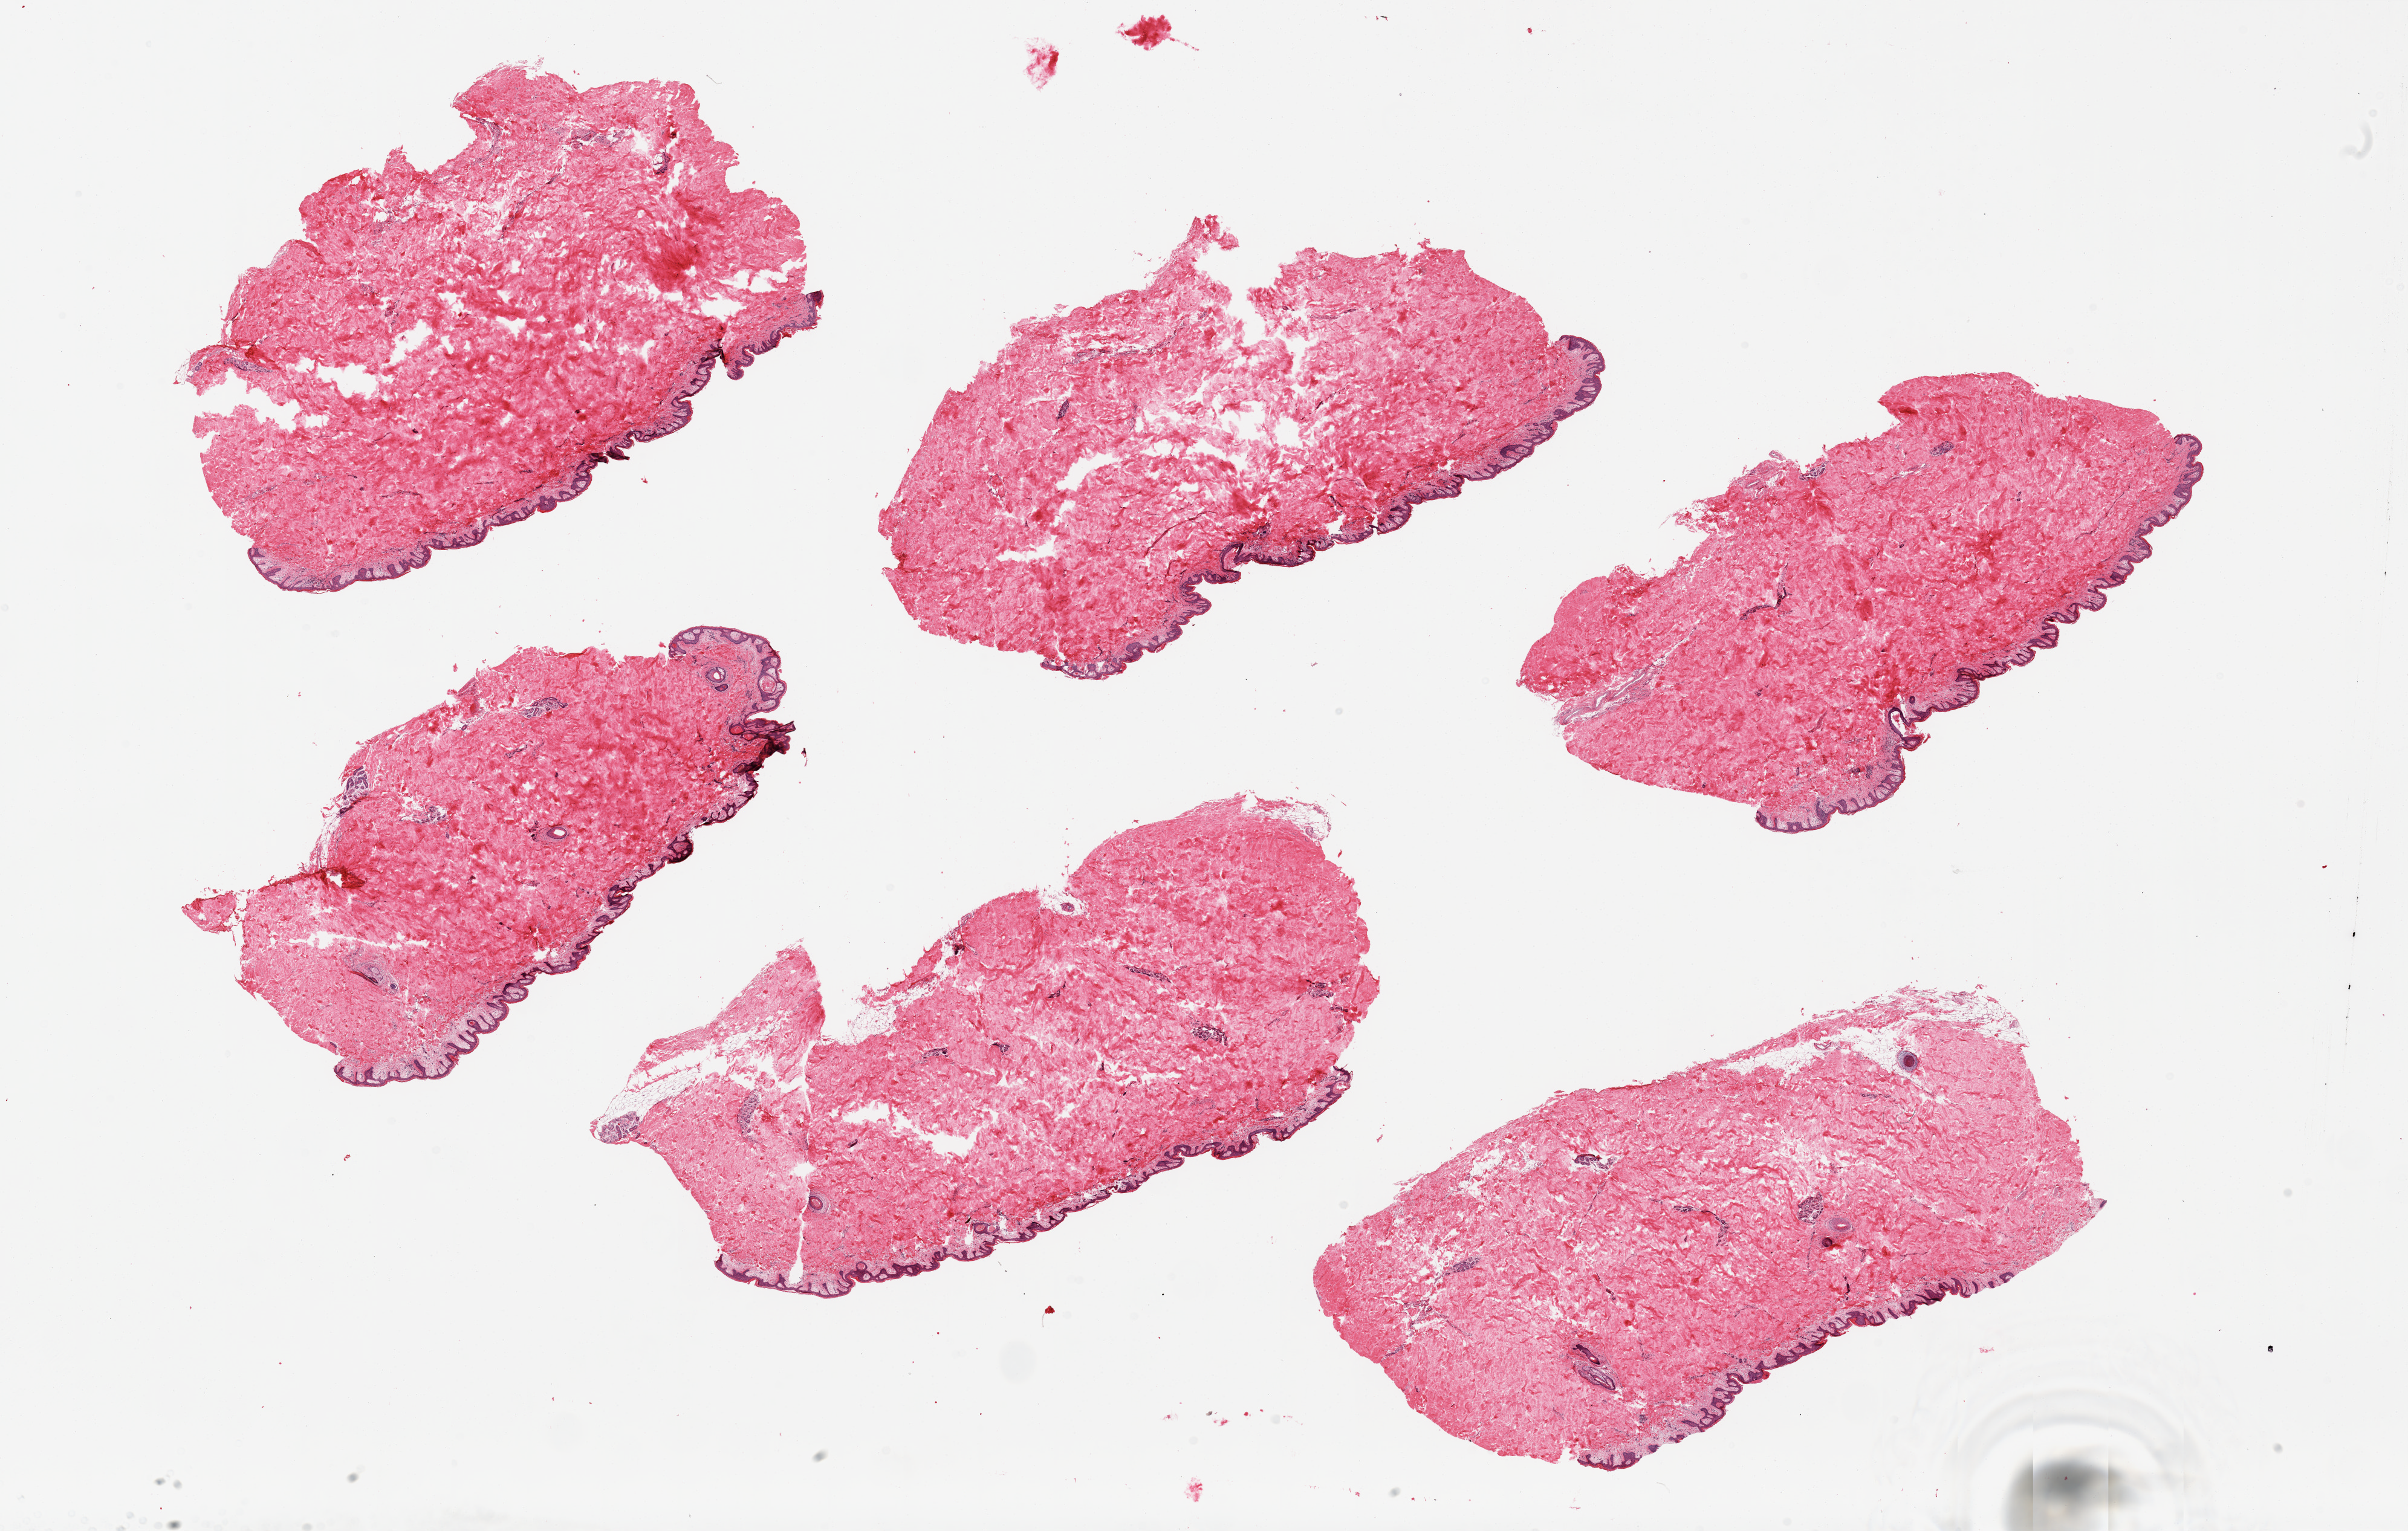
Digitized hematoxylin and eosin (H&E)-stained section, whole scanned area (about 31.5 x 20.0 mm) shown as a low-resolution overview. PAXgene-fixed, paraffin-embedded tissue. Section of skin of suprapubic region (target tissue). Tissue donor sample.
- review note (as recorded): 6 pieces; well trimmed; <1% intradermal fat